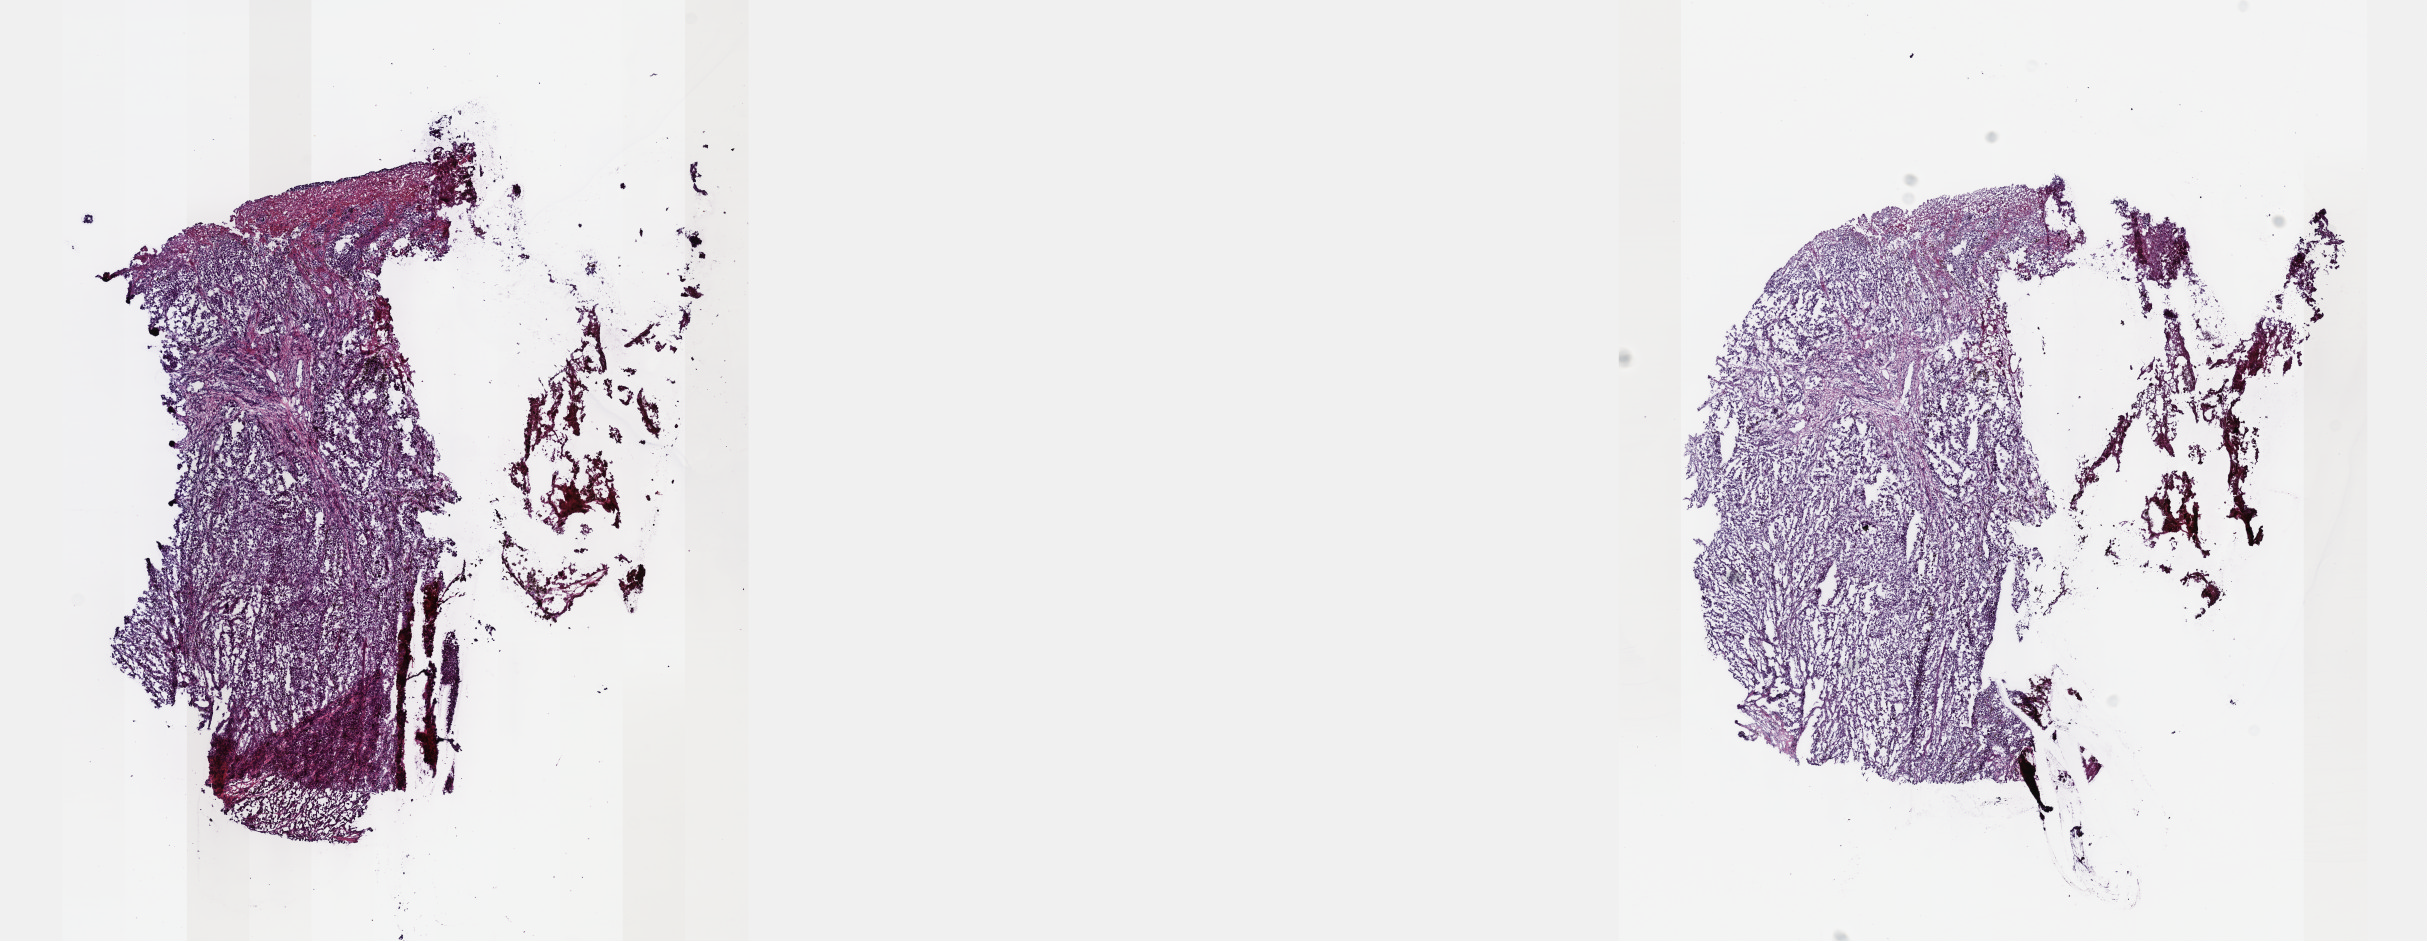
H&E-stained whole-slide image, shown as a low-resolution overview of the whole scanned area (about 19.6 x 7.6 mm, slide scanned at 40x), frozen section, metastatic tumour sample, sampled site not recorded. Female, age 56 years at initial diagnosis. Slide review estimates, as recorded: tumour cells 85%, tumour nuclei 90%, normal cells 0%, stromal cells 15%, necrosis 0%. Inflammatory infiltration, as recorded: lymphocyte infiltration 0%, monocyte infiltration 0%, neutrophil infiltration 0%.
• this section: metastatic tumour tissue
• patient diagnosis: Malignant melanoma, NOS